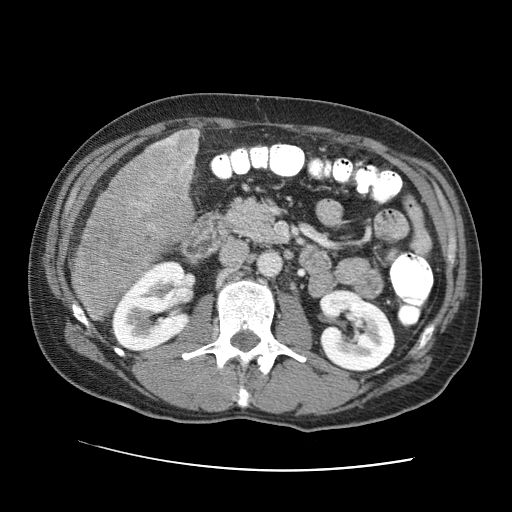
Contrast-enhanced abdominal CT (liver protocol), one axial slice; position 25 of 95 along the scan axis; one of 2 acquisitions stored at this slice position; soft-tissue window (W 400 / L 40 HU); 2.5 mm slice thickness; 512 × 512 image matrix. Case-level facts recorded for this patient, not image findings: diagnosis: hepatocellular carcinoma (patient treated with transarterial chemoembolisation; whether this scan precedes or follows treatment is not stated here); TNM stage (as recorded): Stage-IVA; Child-Pugh class: A; tumour differentiation: moderately differentiated; tumour nodularity: multinodular.
Annotated regions visible in this slice (semi-automatically segmented with operator editing):
- liver parenchyma outside the tumour (the mass and vessels are separate outlines, so this box may not span the whole liver): bounding box [x1, y1, x2, y2] px = [74, 128, 200, 320]
- mass: [69, 128, 197, 321]